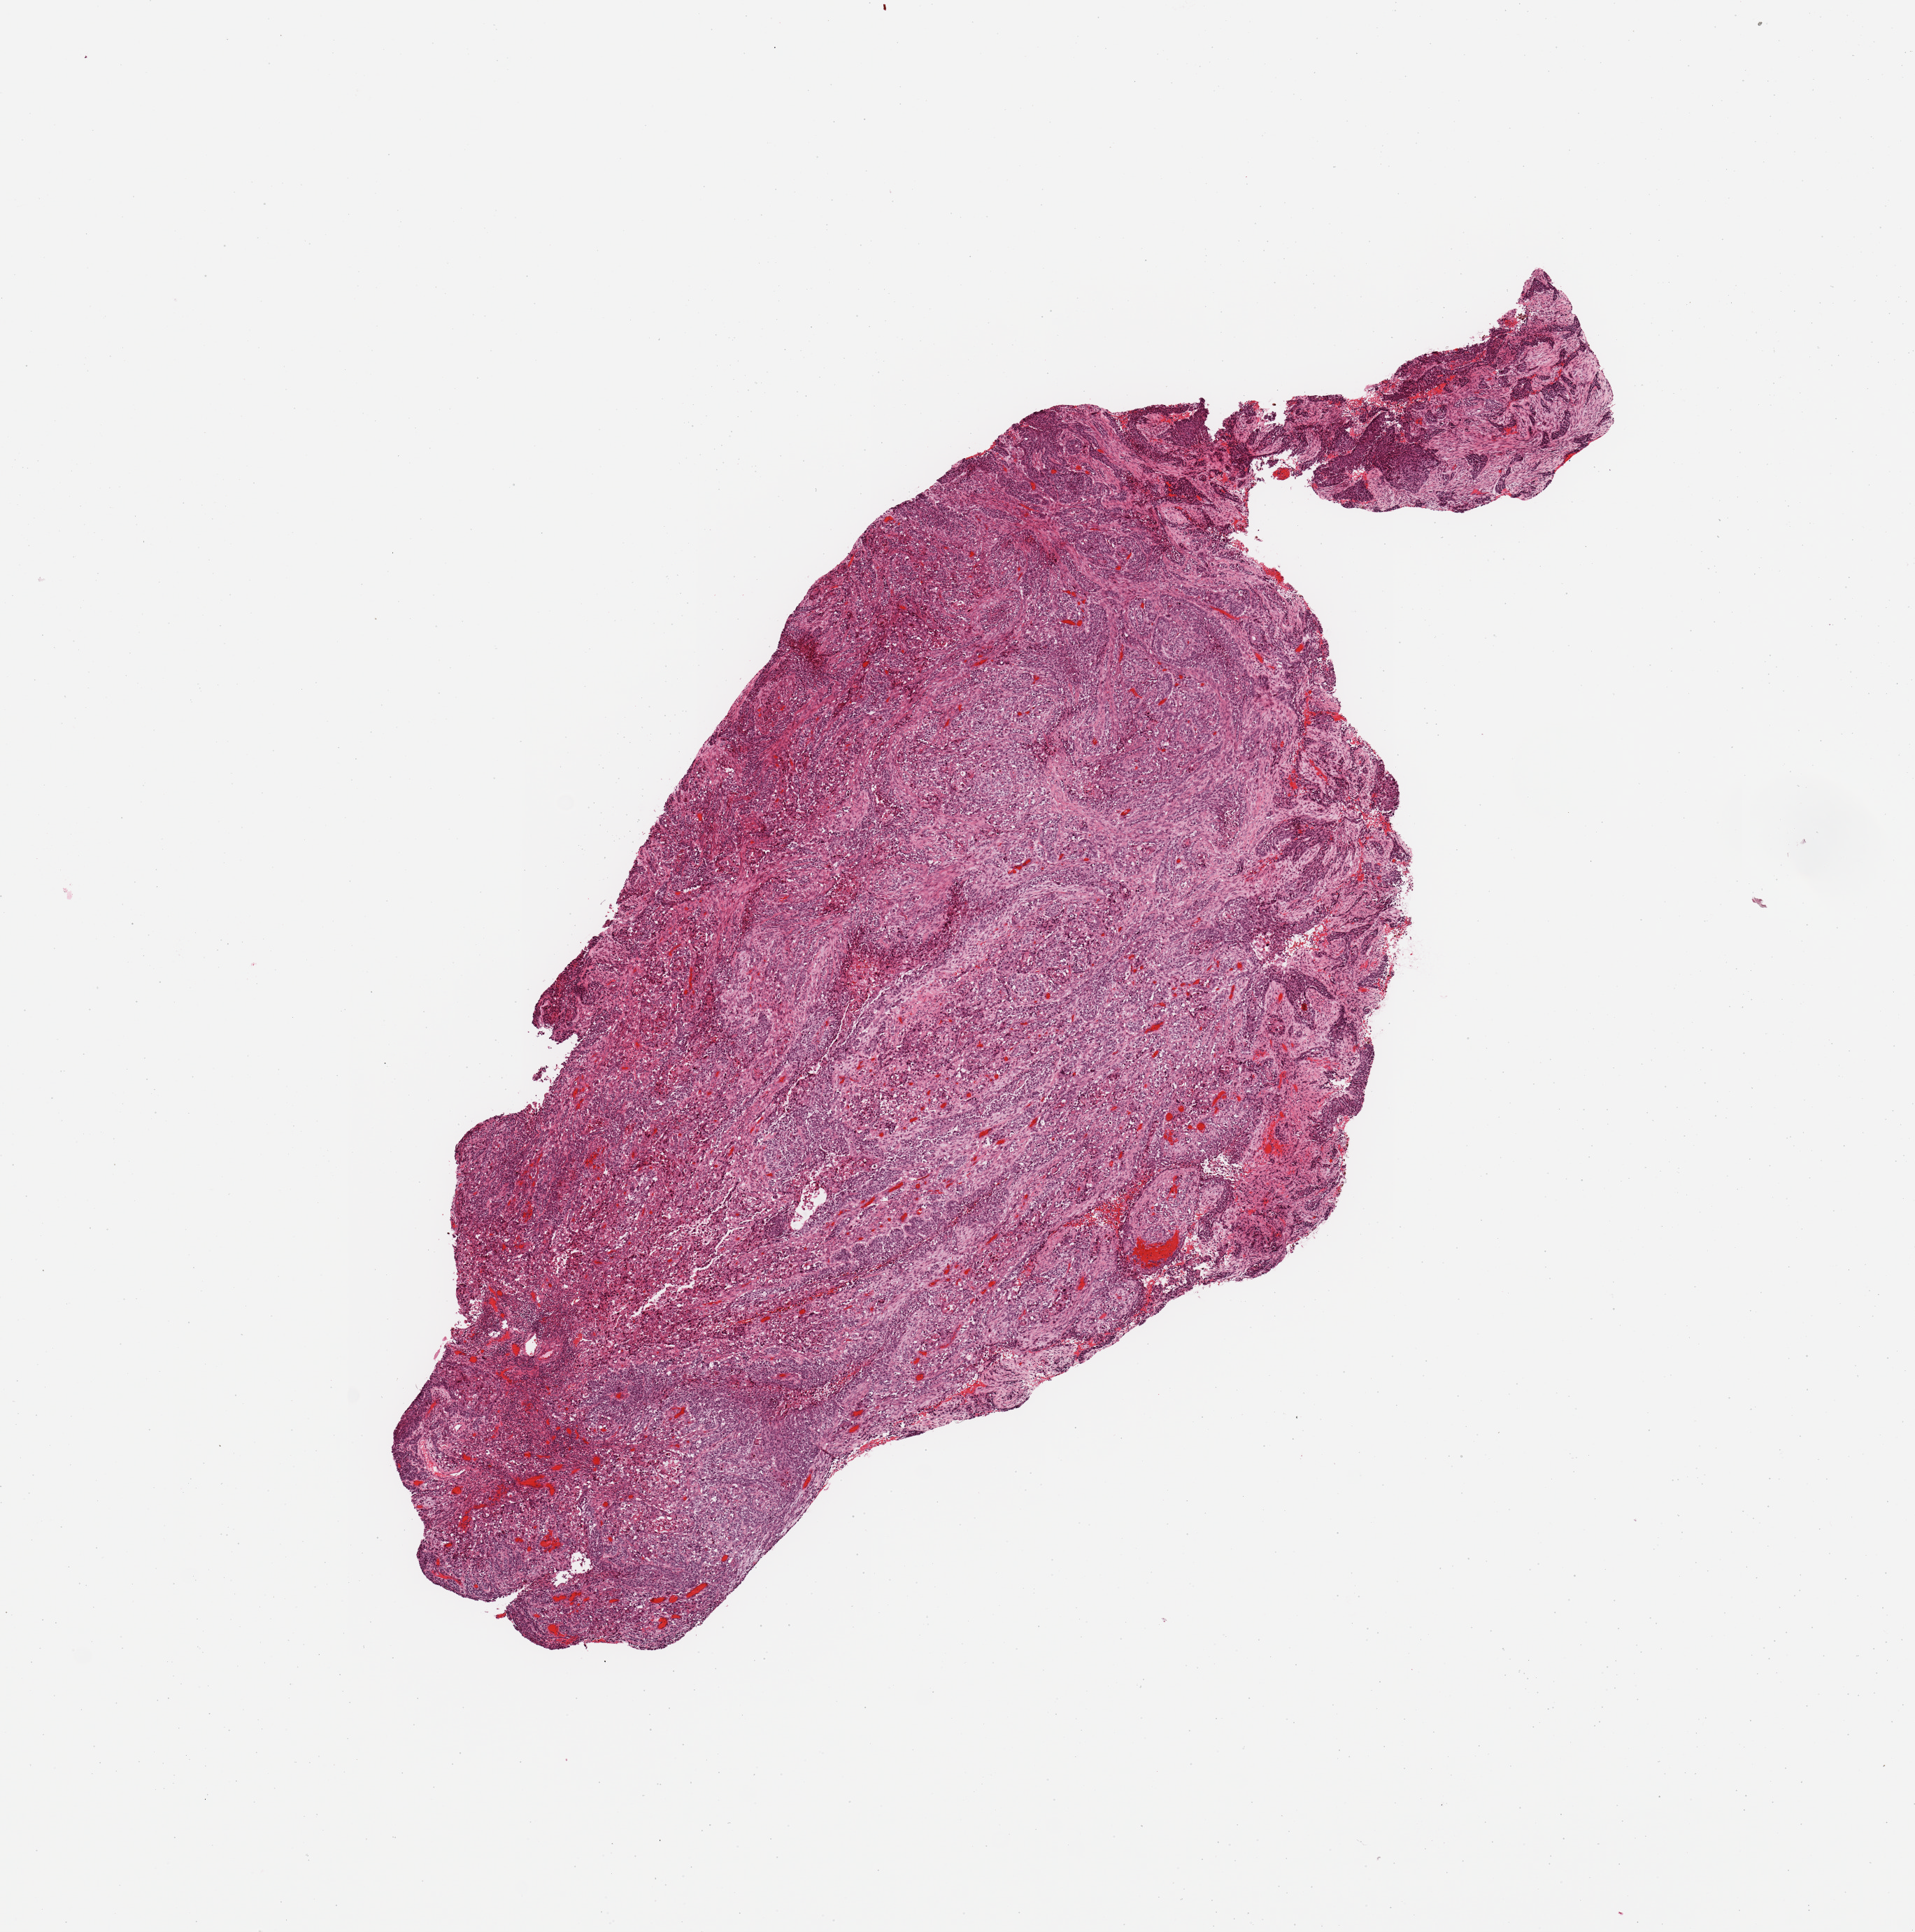
Digitized H&E-stained tissue section (whole slide) — a low-resolution overview of the entire scanned area, about 10.8 x 10.9 mm, tumour tissue sample, lung. Male, 74 y/o.
Histologic diagnosis: Squamous cell carcinoma, NOS.